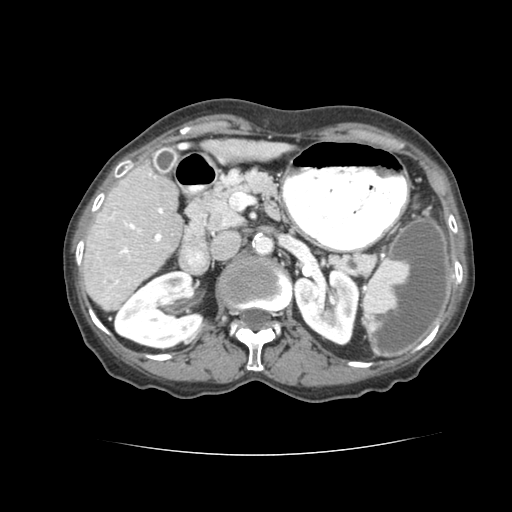
Contrast-enhanced abdominal CT (liver protocol), one axial slice; soft-tissue window (W 400 / L 40 HU); 2.5 mm slice thickness; 512 × 512 image matrix, field of view 340 × 340 mm. From the clinical record (not read from this slice): diagnosis: hepatocellular carcinoma (patient treated with transarterial chemoembolisation; whether this scan precedes or follows treatment is not stated here); TNM stage (as recorded): Stage-I; Child-Pugh class: A; tumour differentiation: well differentiated; tumour nodularity: uninodular.
Annotated regions visible in this slice (semi-automatic segmentation, software-assisted and operator-edited):
- liver parenchyma outside the tumour (the mass and vessels are separate outlines, so this box may not span the whole liver): box from (x=80, y=146) to (x=283, y=310) px
- liver vessels: (x=104, y=166)–(x=163, y=277)